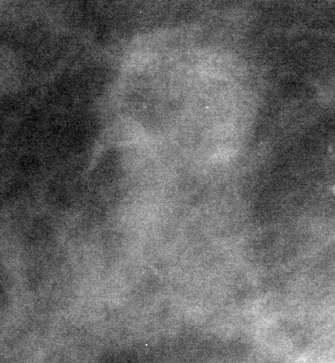
Region of interest cut from a scanned film mammogram (one marked finding); right breast; MLO view.
- Finding: mass, shape round, margins obscured; BI-RADS assessment category 3; pathology result (as recorded, not read from the image): benign.